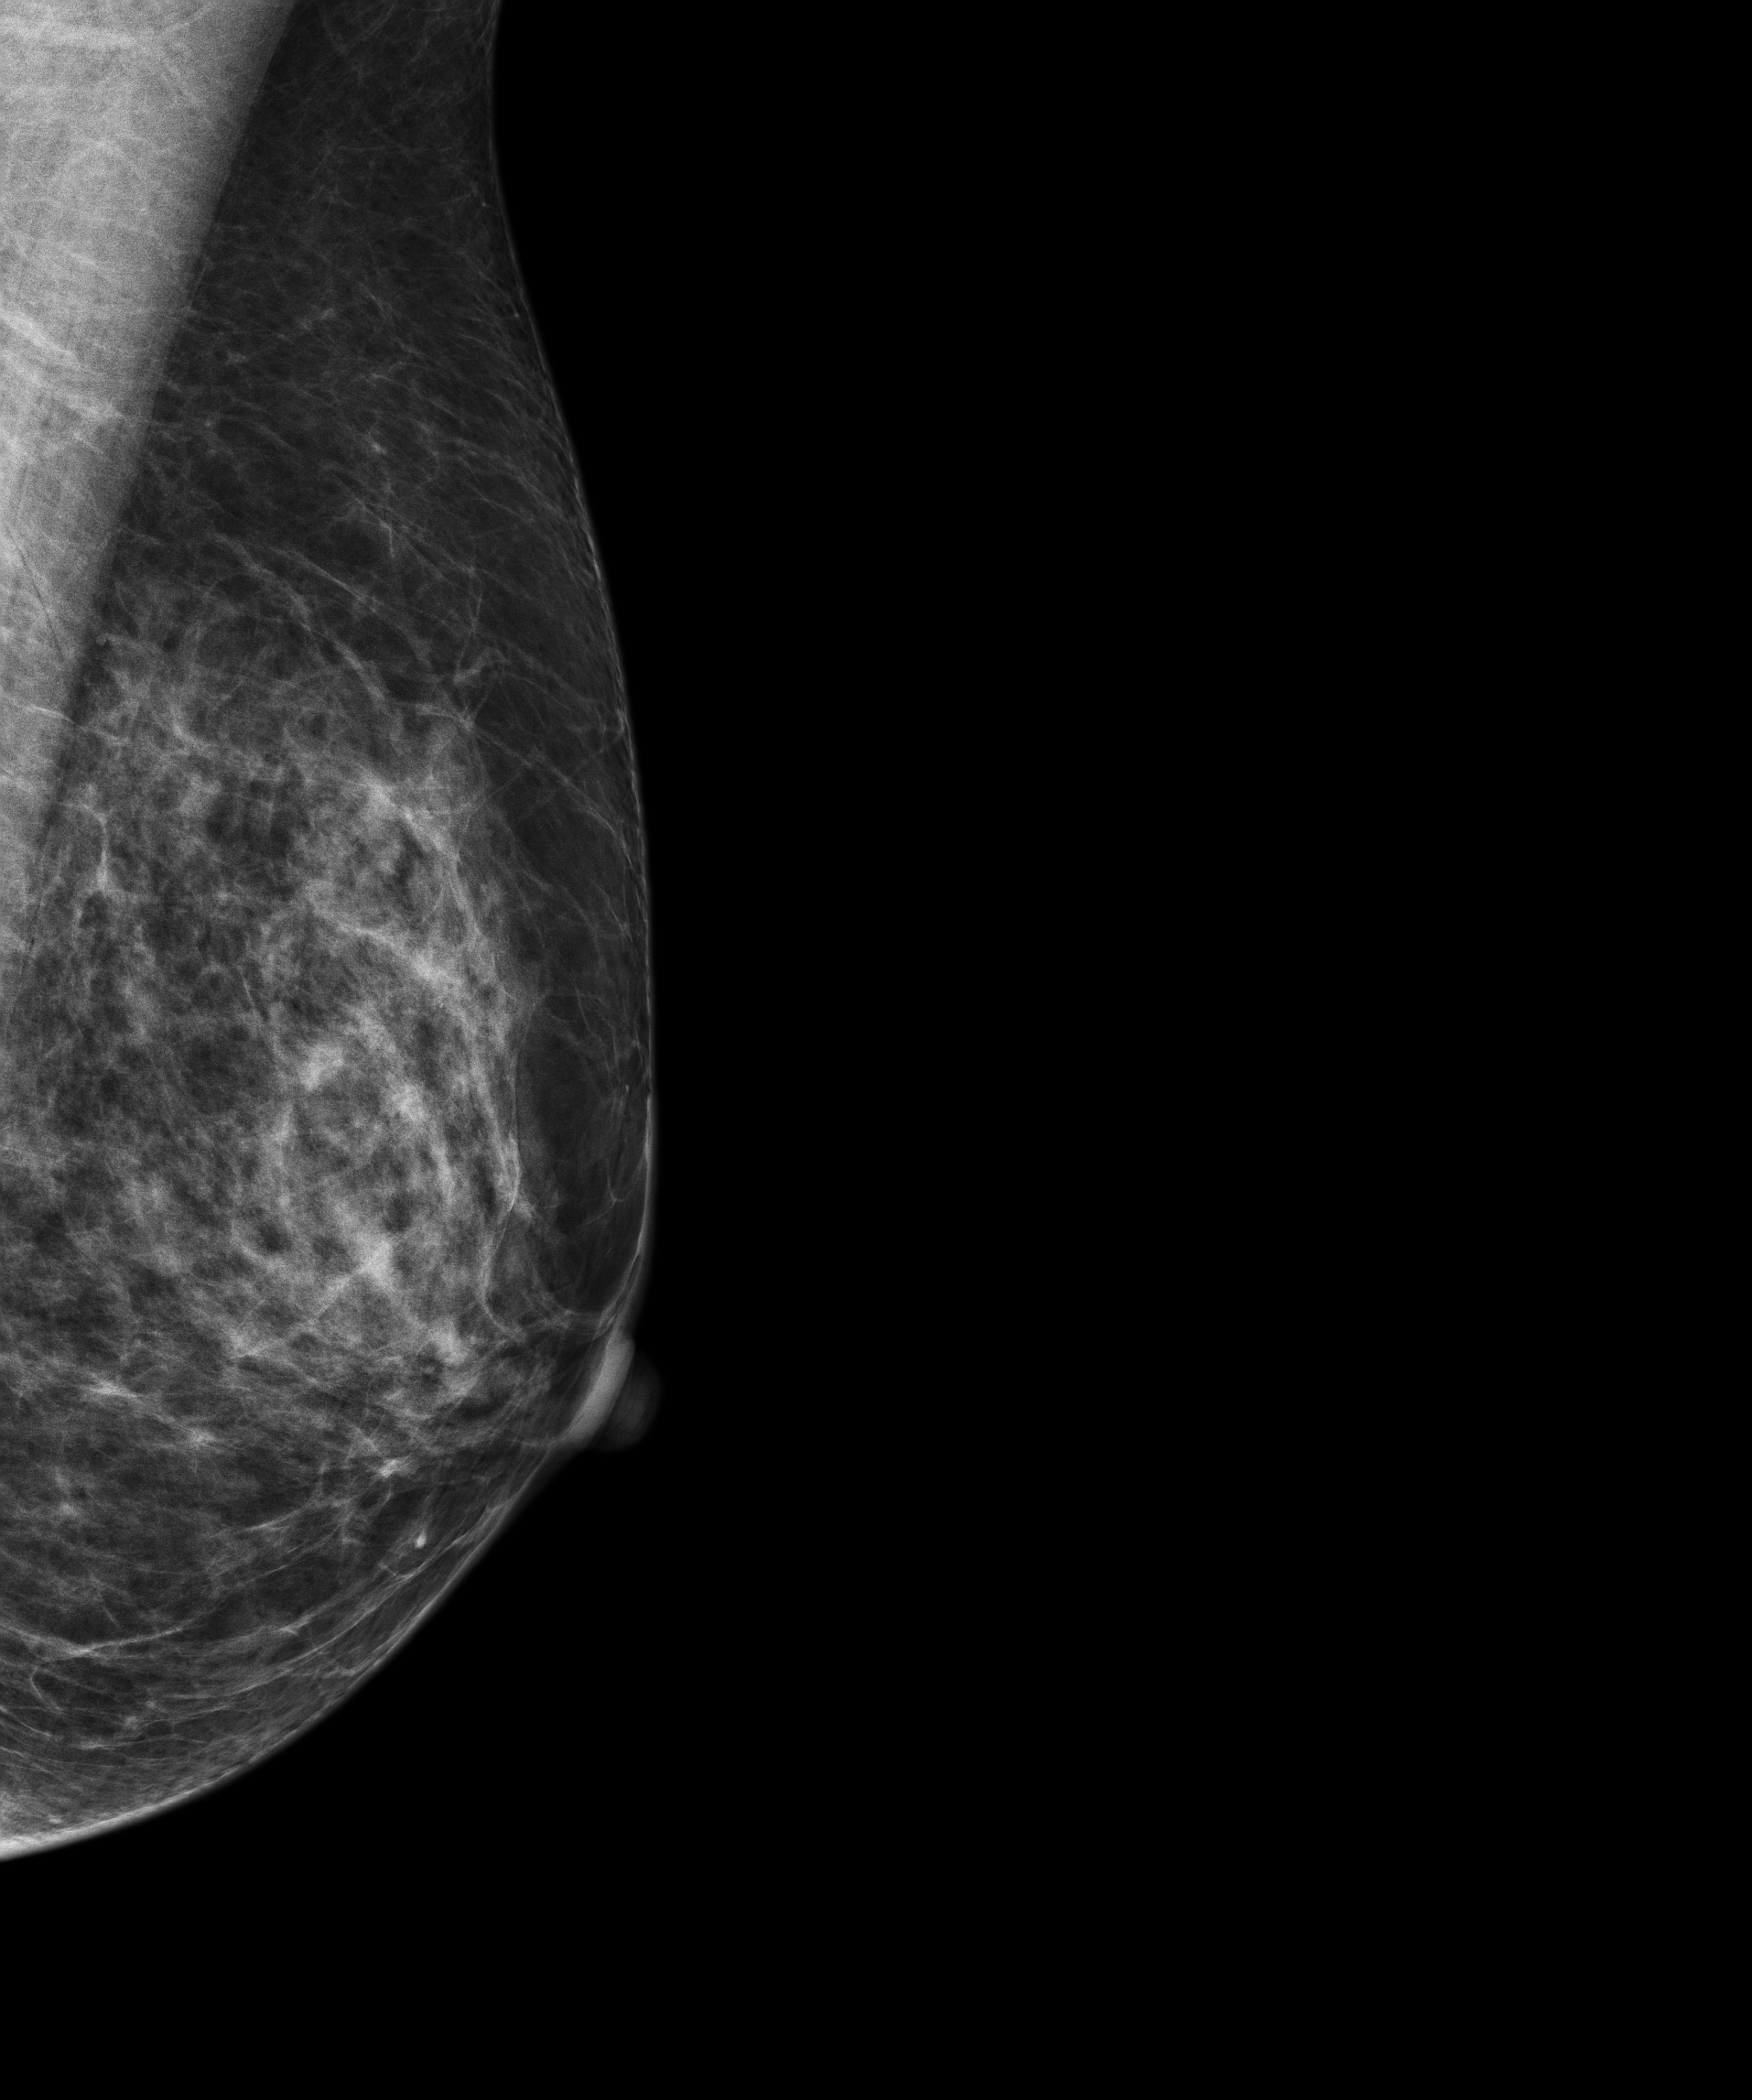
Annual screening mammography examination. Patient: female, 61 years.
Image type: full-field digital mammogram. Breast: left. Projection: medio-lateral oblique projection.